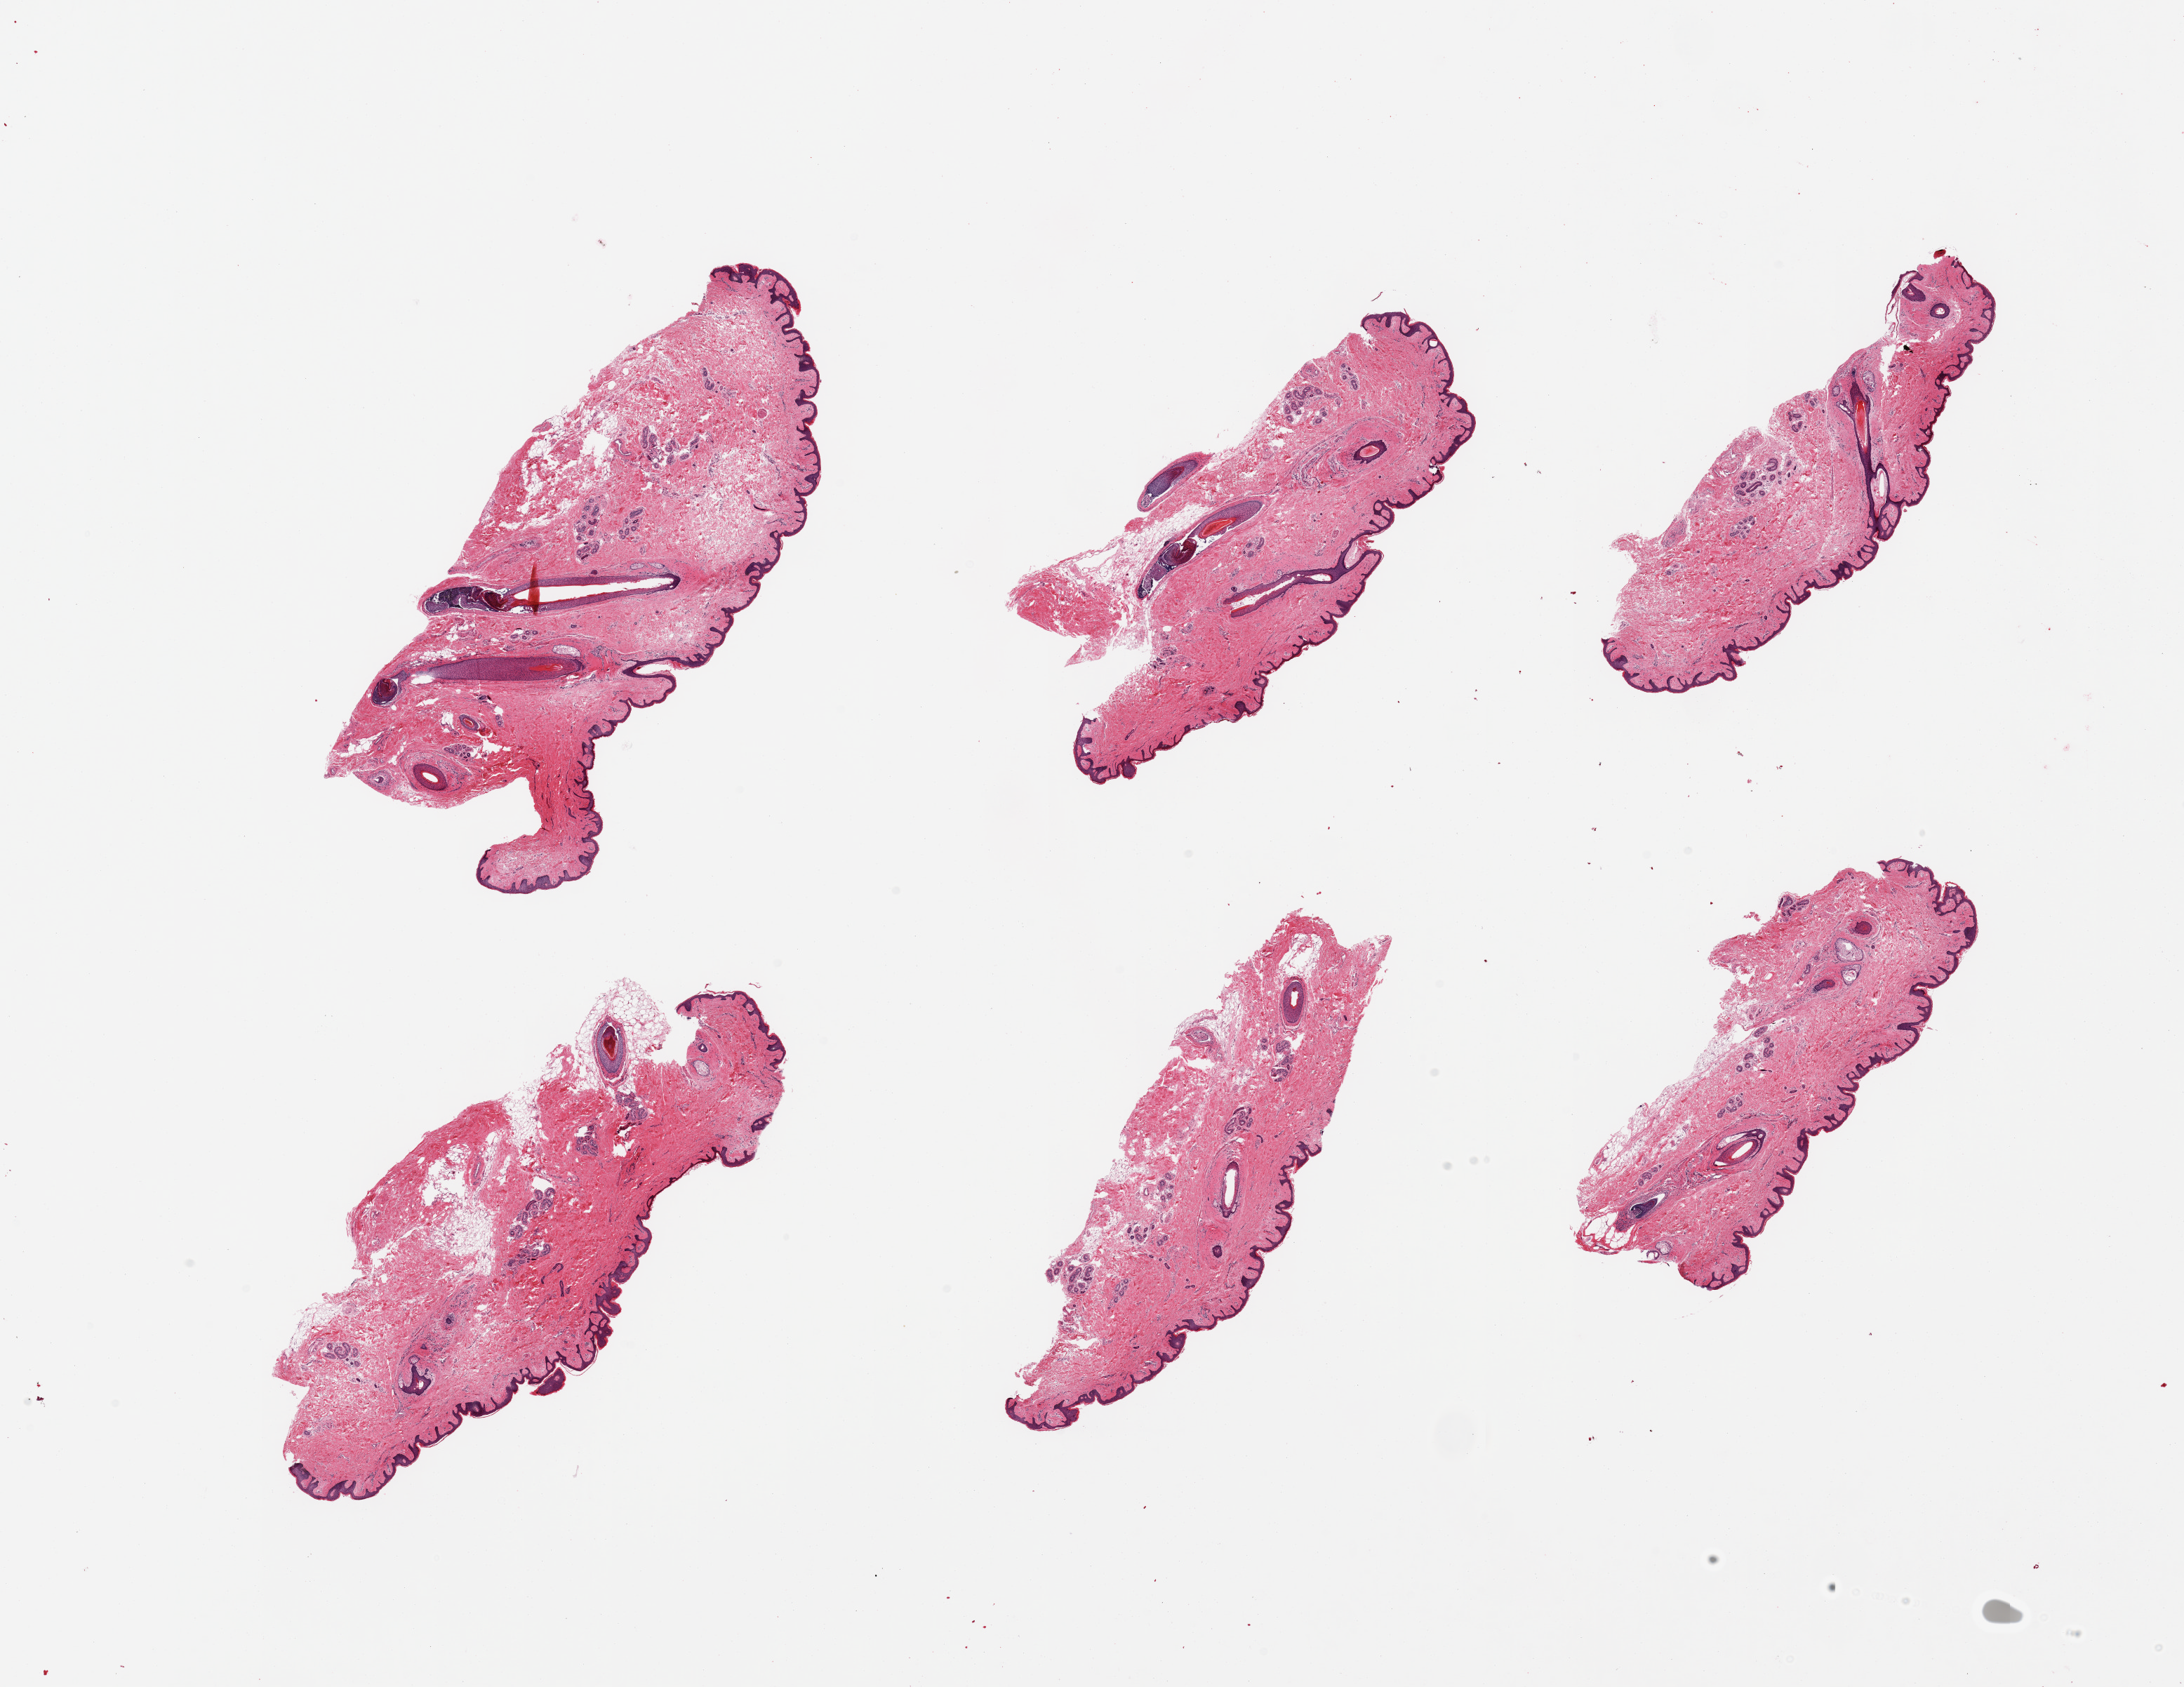
Whole-slide image, hematoxylin and eosin (H&E) stain, brightfield, low-resolution overview of the scanned area, about 24.6 x 19.0 mm (acquisition: 20x scan), PAXgene-fixed, paraffin-embedded tissue, target tissue: skin of suprapubic region, donor tissue sample.
Pathologist's review note for this sample: 6 pieces; well trimmed, but prominent hair follicles.